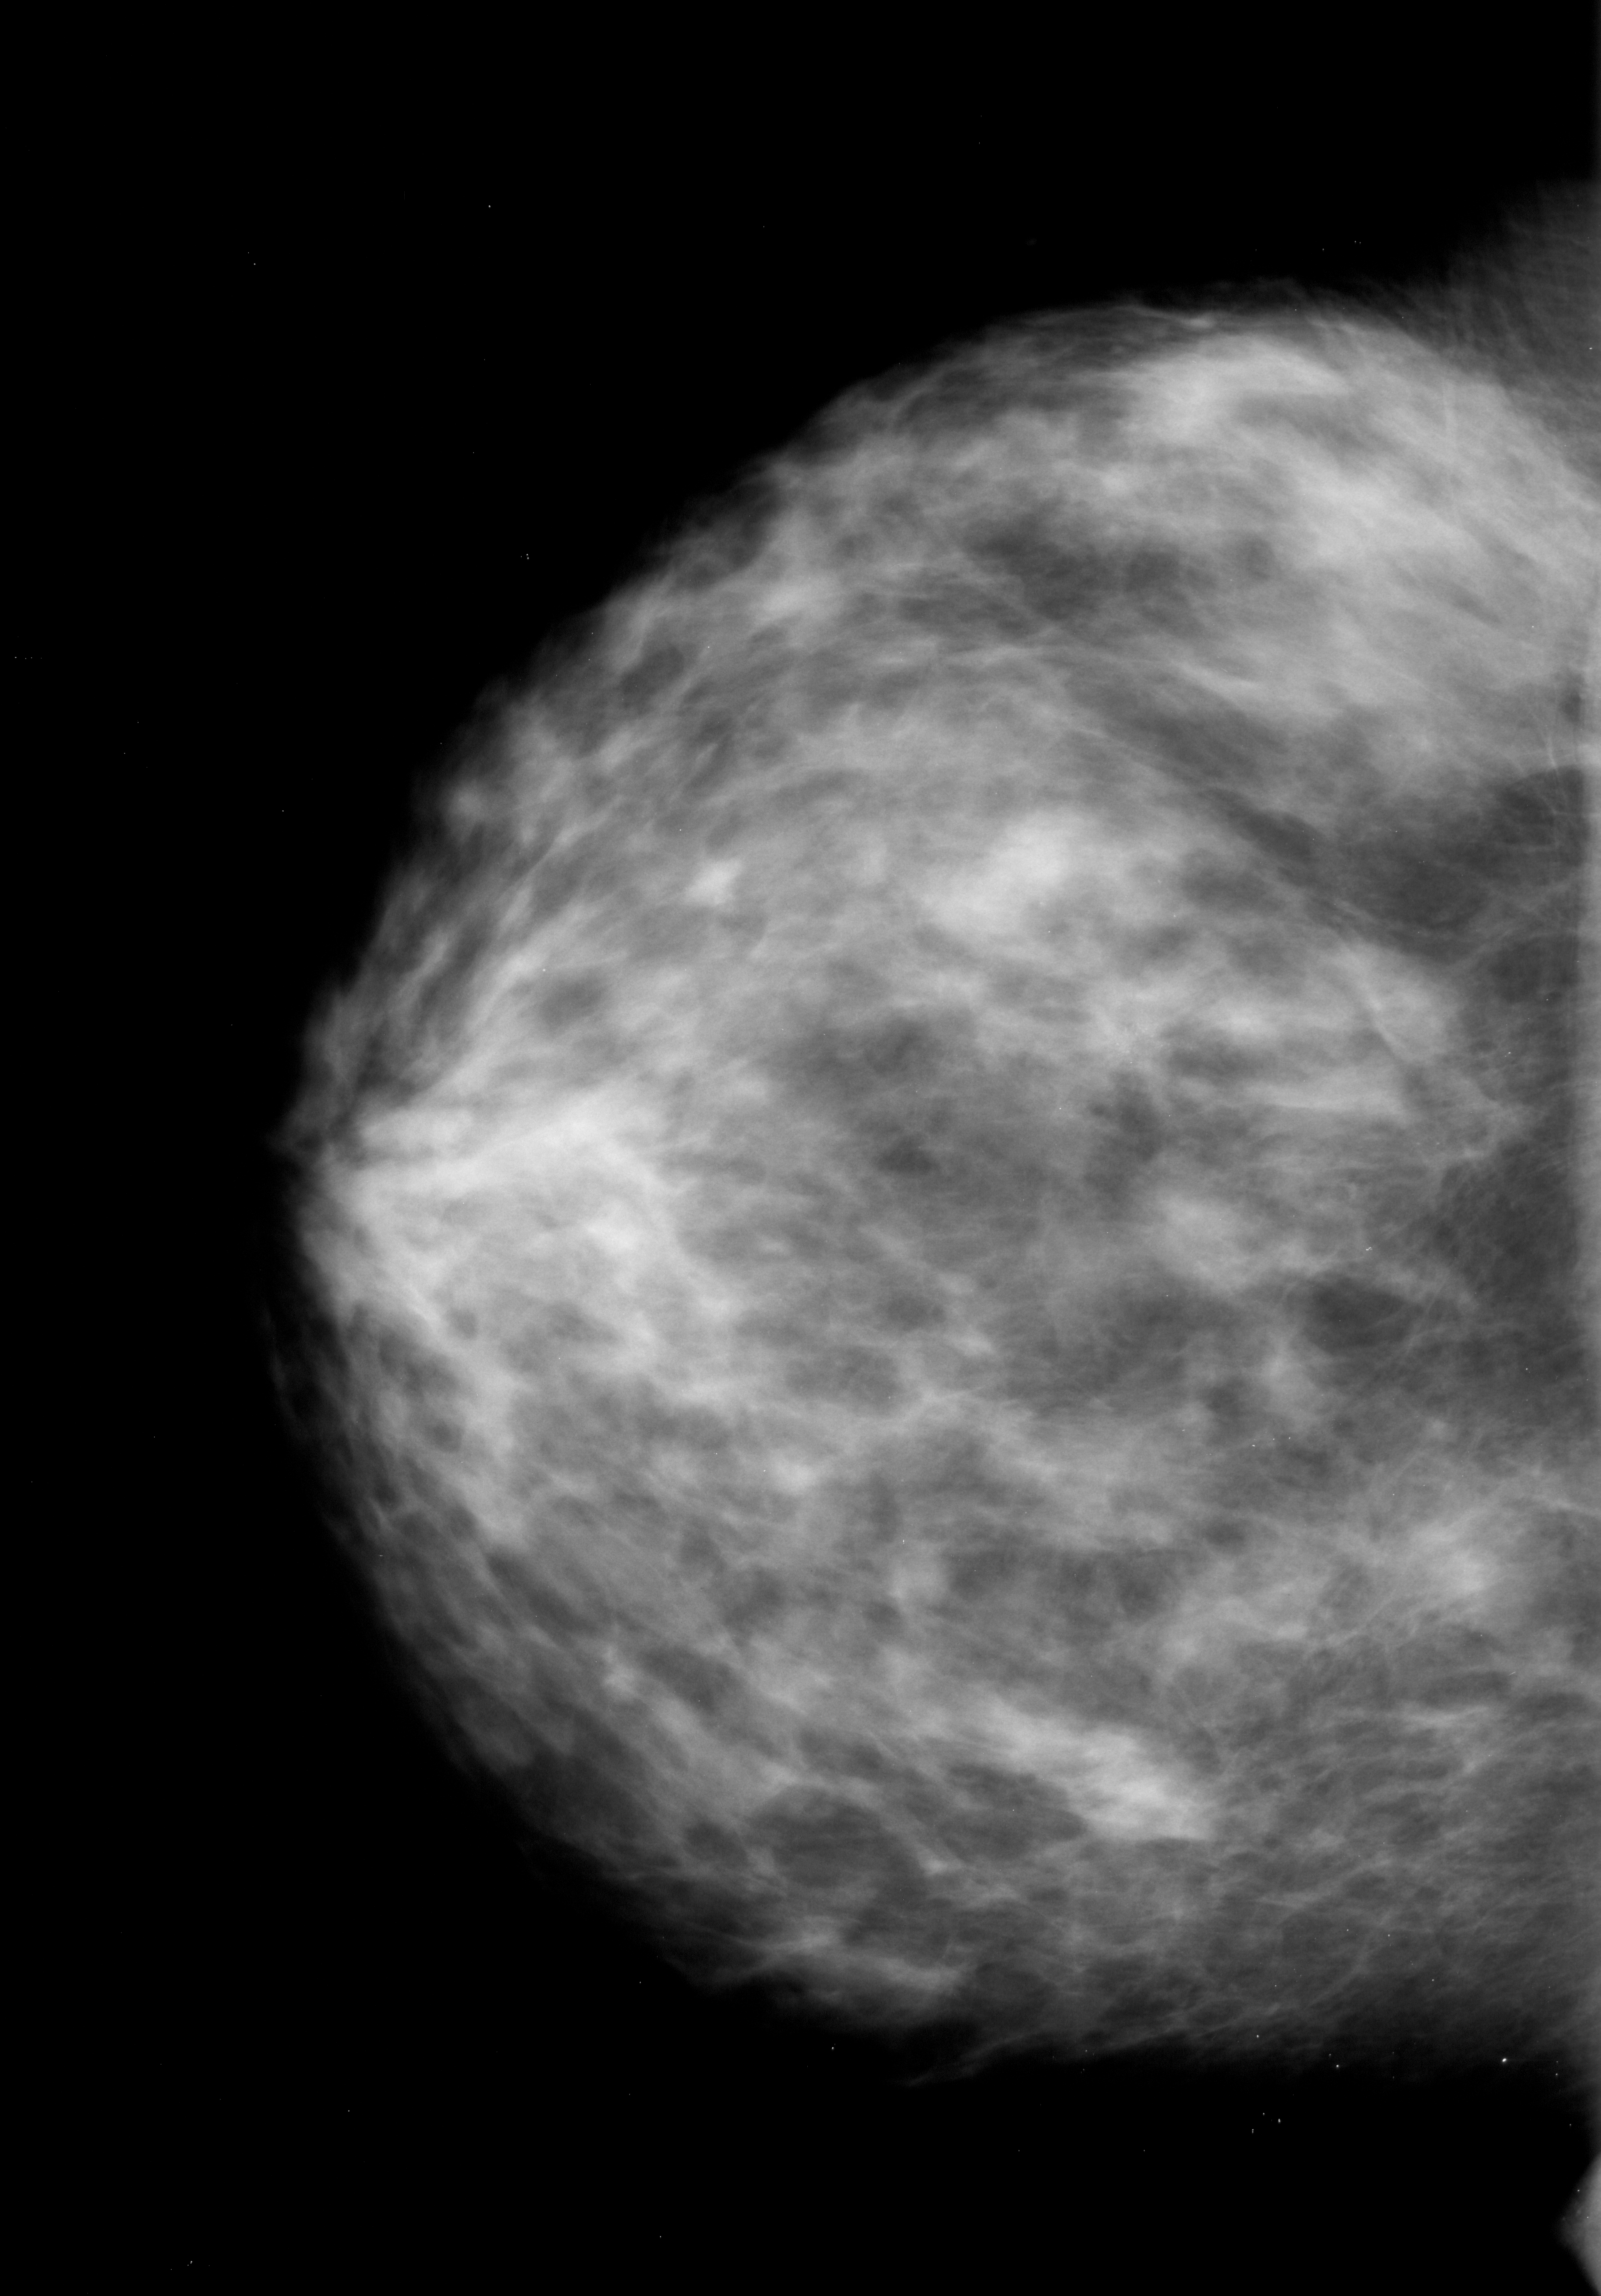
Mammogram (digitized film), left breast, craniocaudal (CC) view, breast composition: extremely dense (BI-RADS density category 4 of 4).
Abnormality record for this image: calcifications, morphology pleomorphic, distribution clustered; BI-RADS assessment category 4; pathology result (as recorded, not read from the image): malignant.